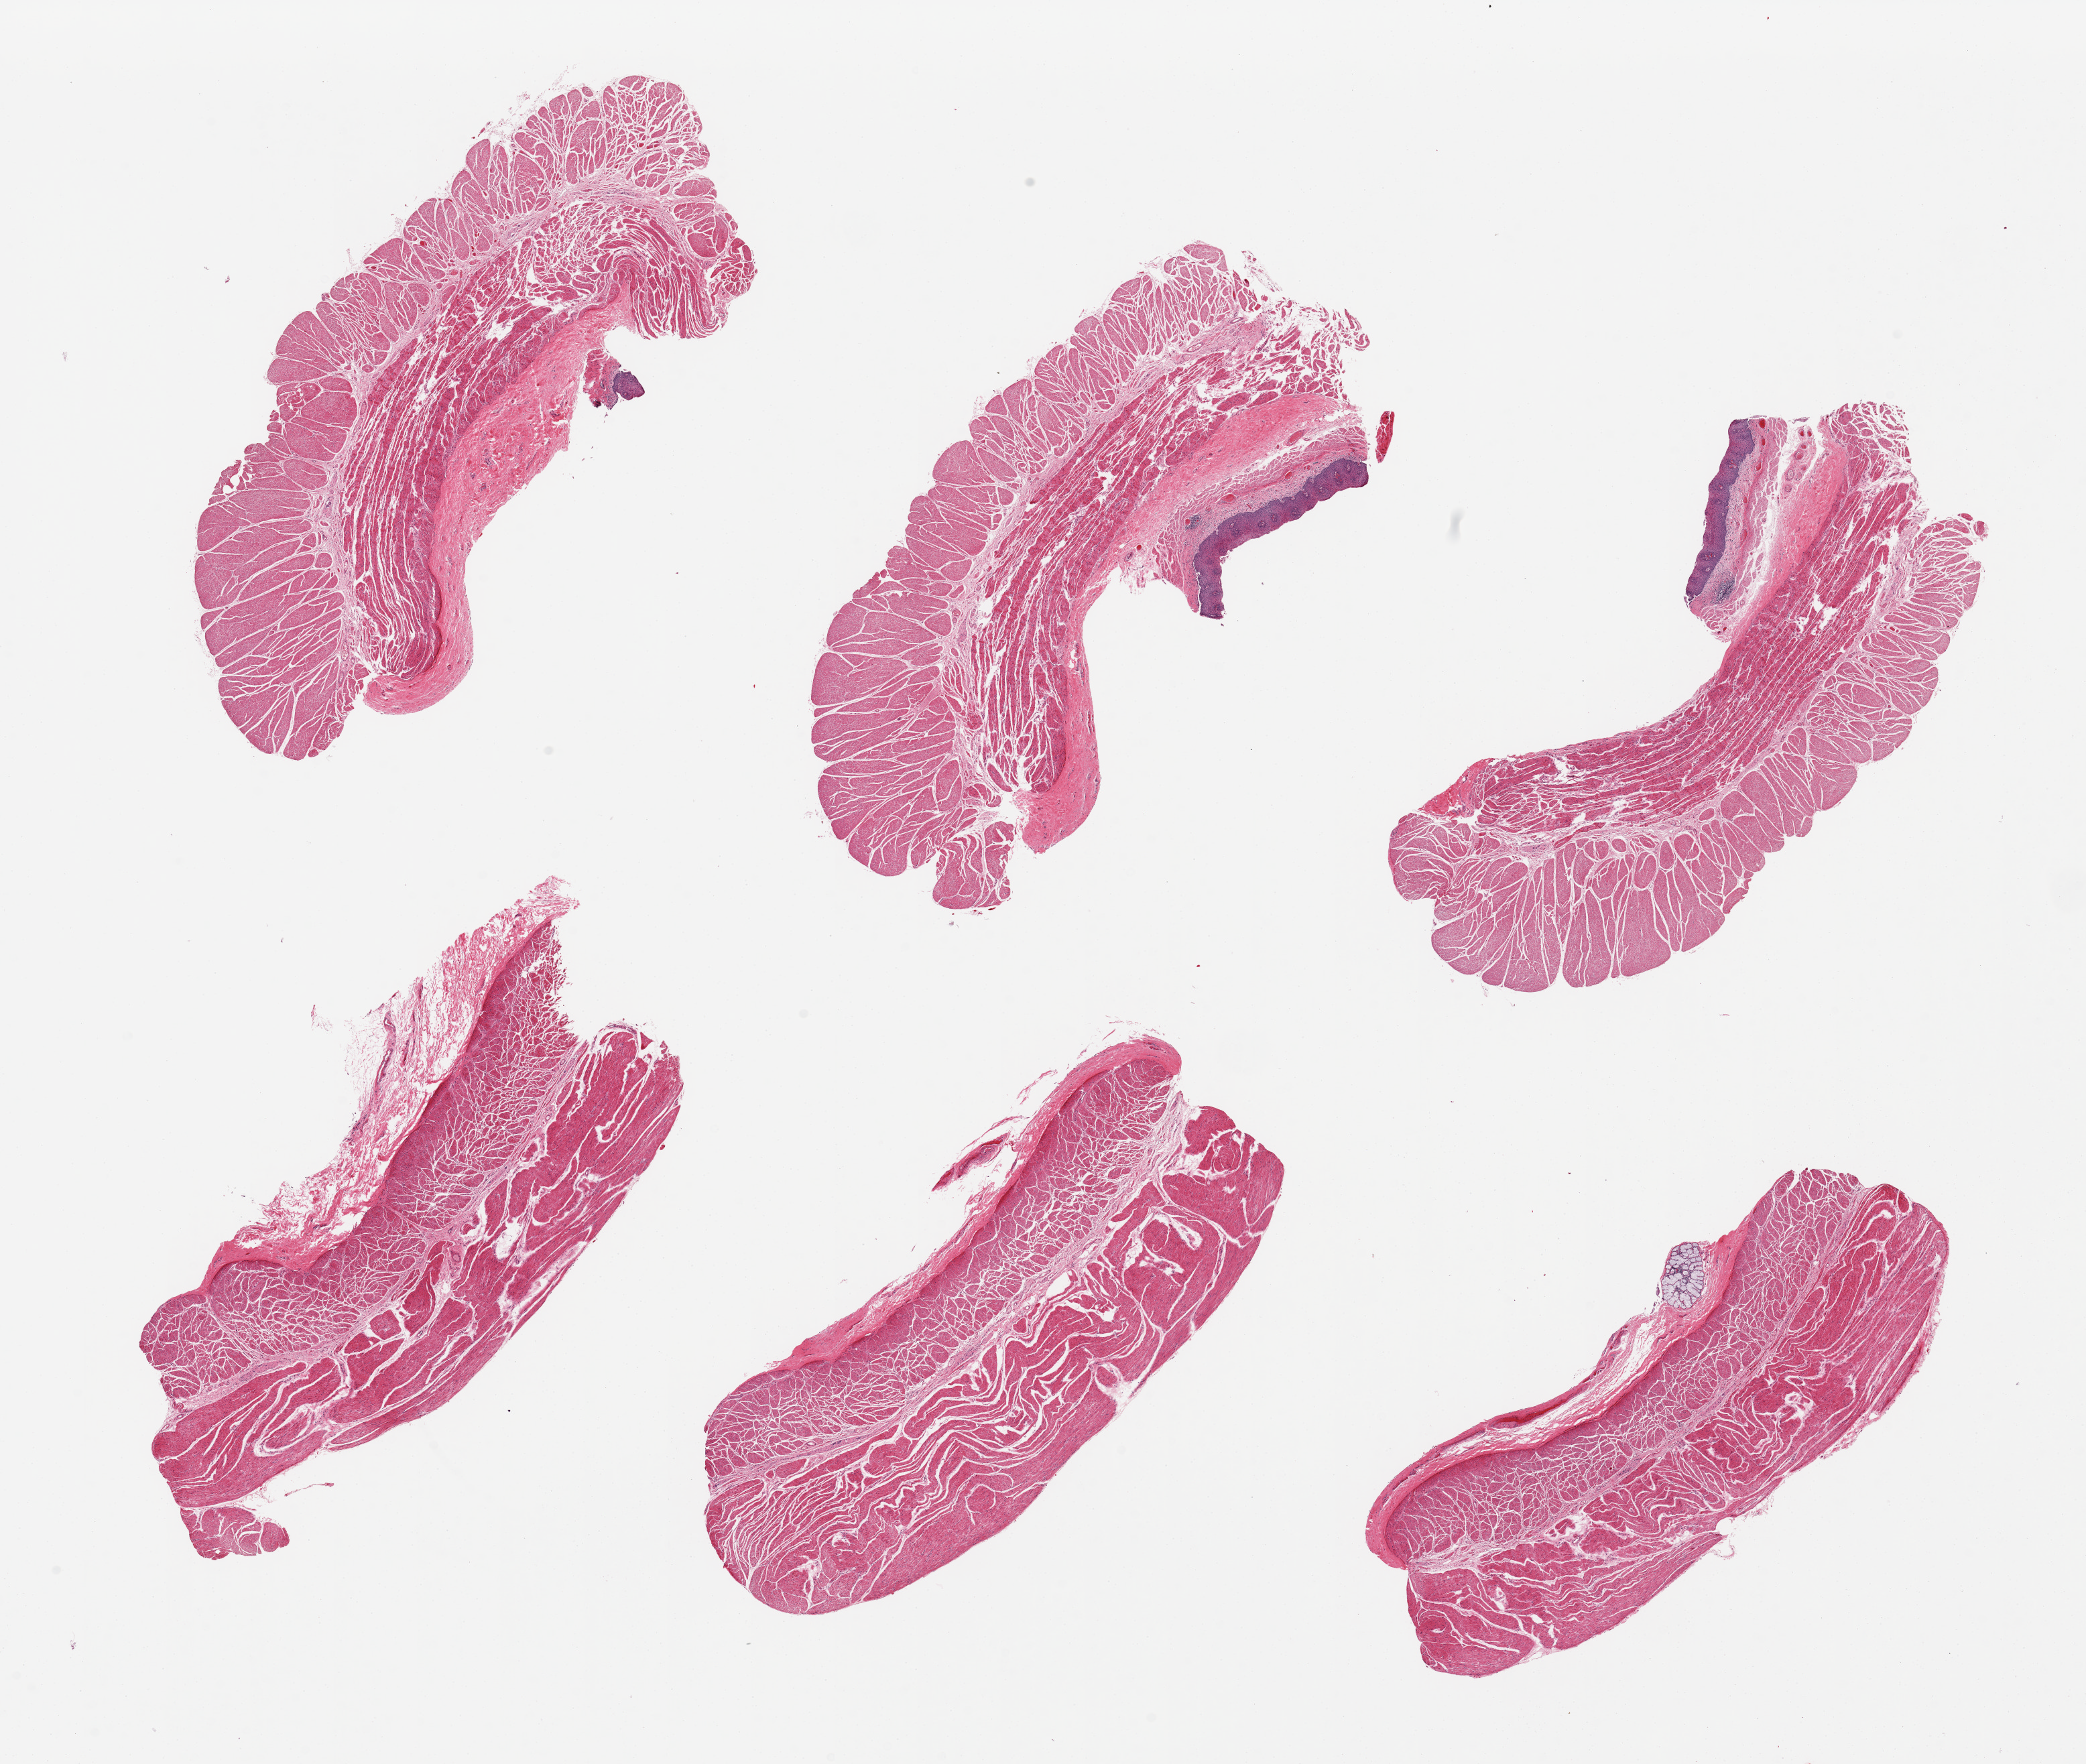
H&E whole-slide image — low-resolution overview of the scanned area, about 24.6 x 20.8 mm. PAXgene-fixed, paraffin-embedded tissue. Section of esophageal muscle (target tissue). Tissue donor sample. Male donor.
Reviewer comment on this tissue sample: 6 pieces; Well trimmed except for 3 mucosal remnants.